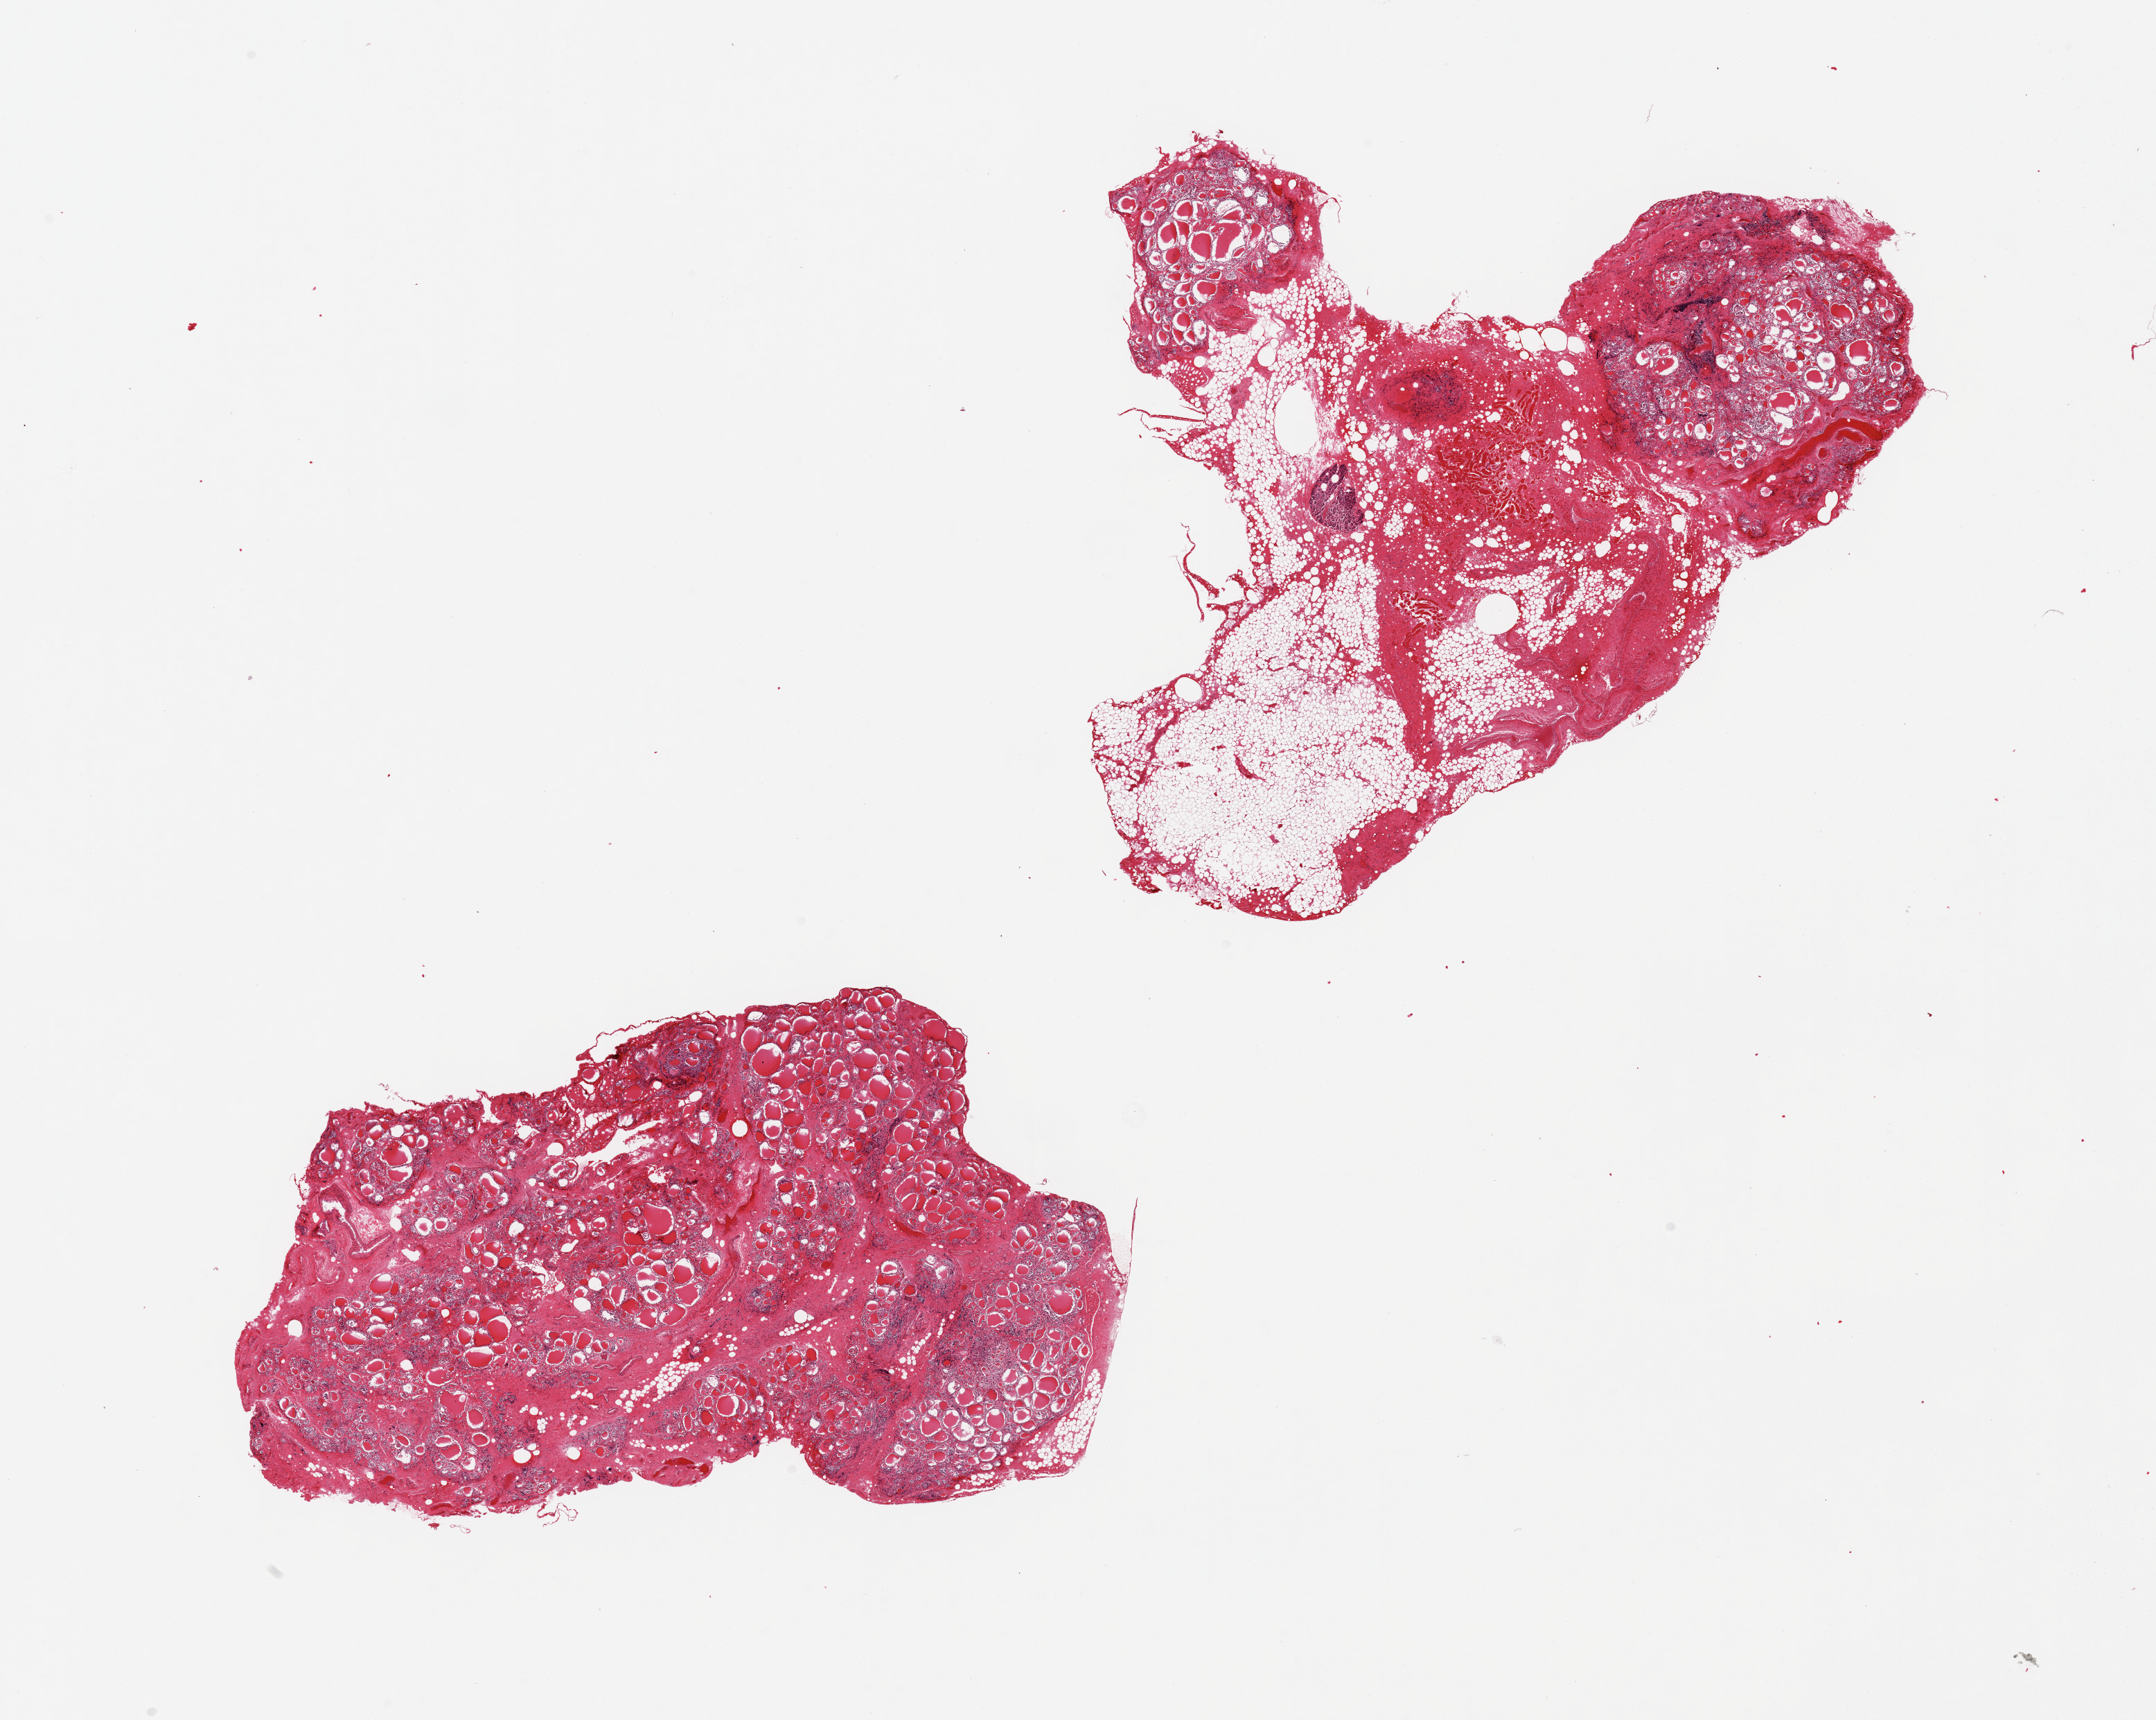
H&E whole-slide image, brightfield — whole scanned area (about 24.6 x 19.6 mm, slide scanned at 20x) shown as a low-resolution overview. PAXgene-fixed paraffin-embedded (PFPE) section. Target tissue: thyroid. Tissue donor sample. Donor sex: female.
* review note (as recorded): 2 pieces; 1, 80% fat and piece of parathyroid; Other piece, nodular with poor preservation